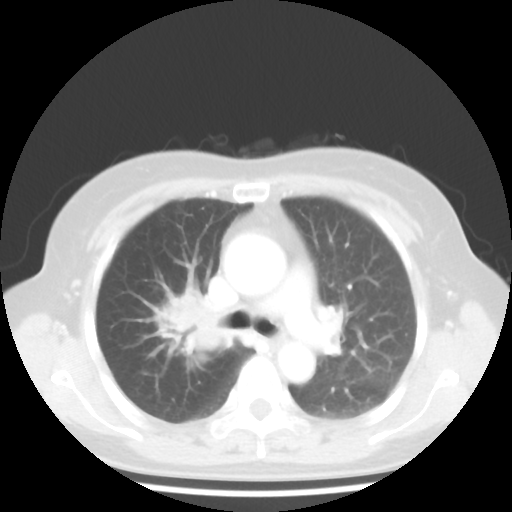
Chest CT, one axial slice. Slice 28 of 44 in the series (ordered by position). 100 kVp. Lung window (W 1500 / L -600 HU). 5 mm slice thickness. 512 × 512 image matrix. Female patient, age 62 years. Case-level facts recorded for this patient, not image findings: clinical TNM (as recorded): T3 N0 M0.
Annotated regions visible in this slice (rectangle marked by the reading radiologist):
- lung tumour (recorded histology: small cell carcinoma): box from (x=145, y=281) to (x=223, y=361) px